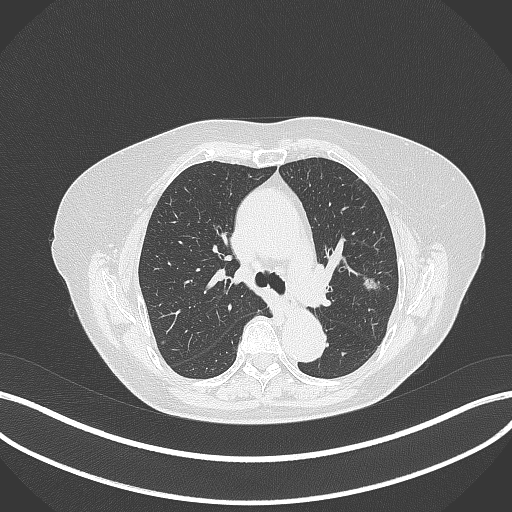
Chest CT, one axial slice; position 217 of 316 along the scan axis; reconstruction kernel B70f; lung window (W 1500 / L -600 HU); 1 mm slice thickness; 512 × 512 image matrix, field of view 400 × 400 mm. Patient: female, 75 years. From the clinical record (not read from this slice): clinical TNM (as recorded): T1c N0 M0.
Annotated regions visible in this slice (rectangle marked by the reading radiologist):
- lung tumour (recorded histology: adenocarcinoma): bounding box <360,275,380,292> (left, top, right, bottom; pixels)